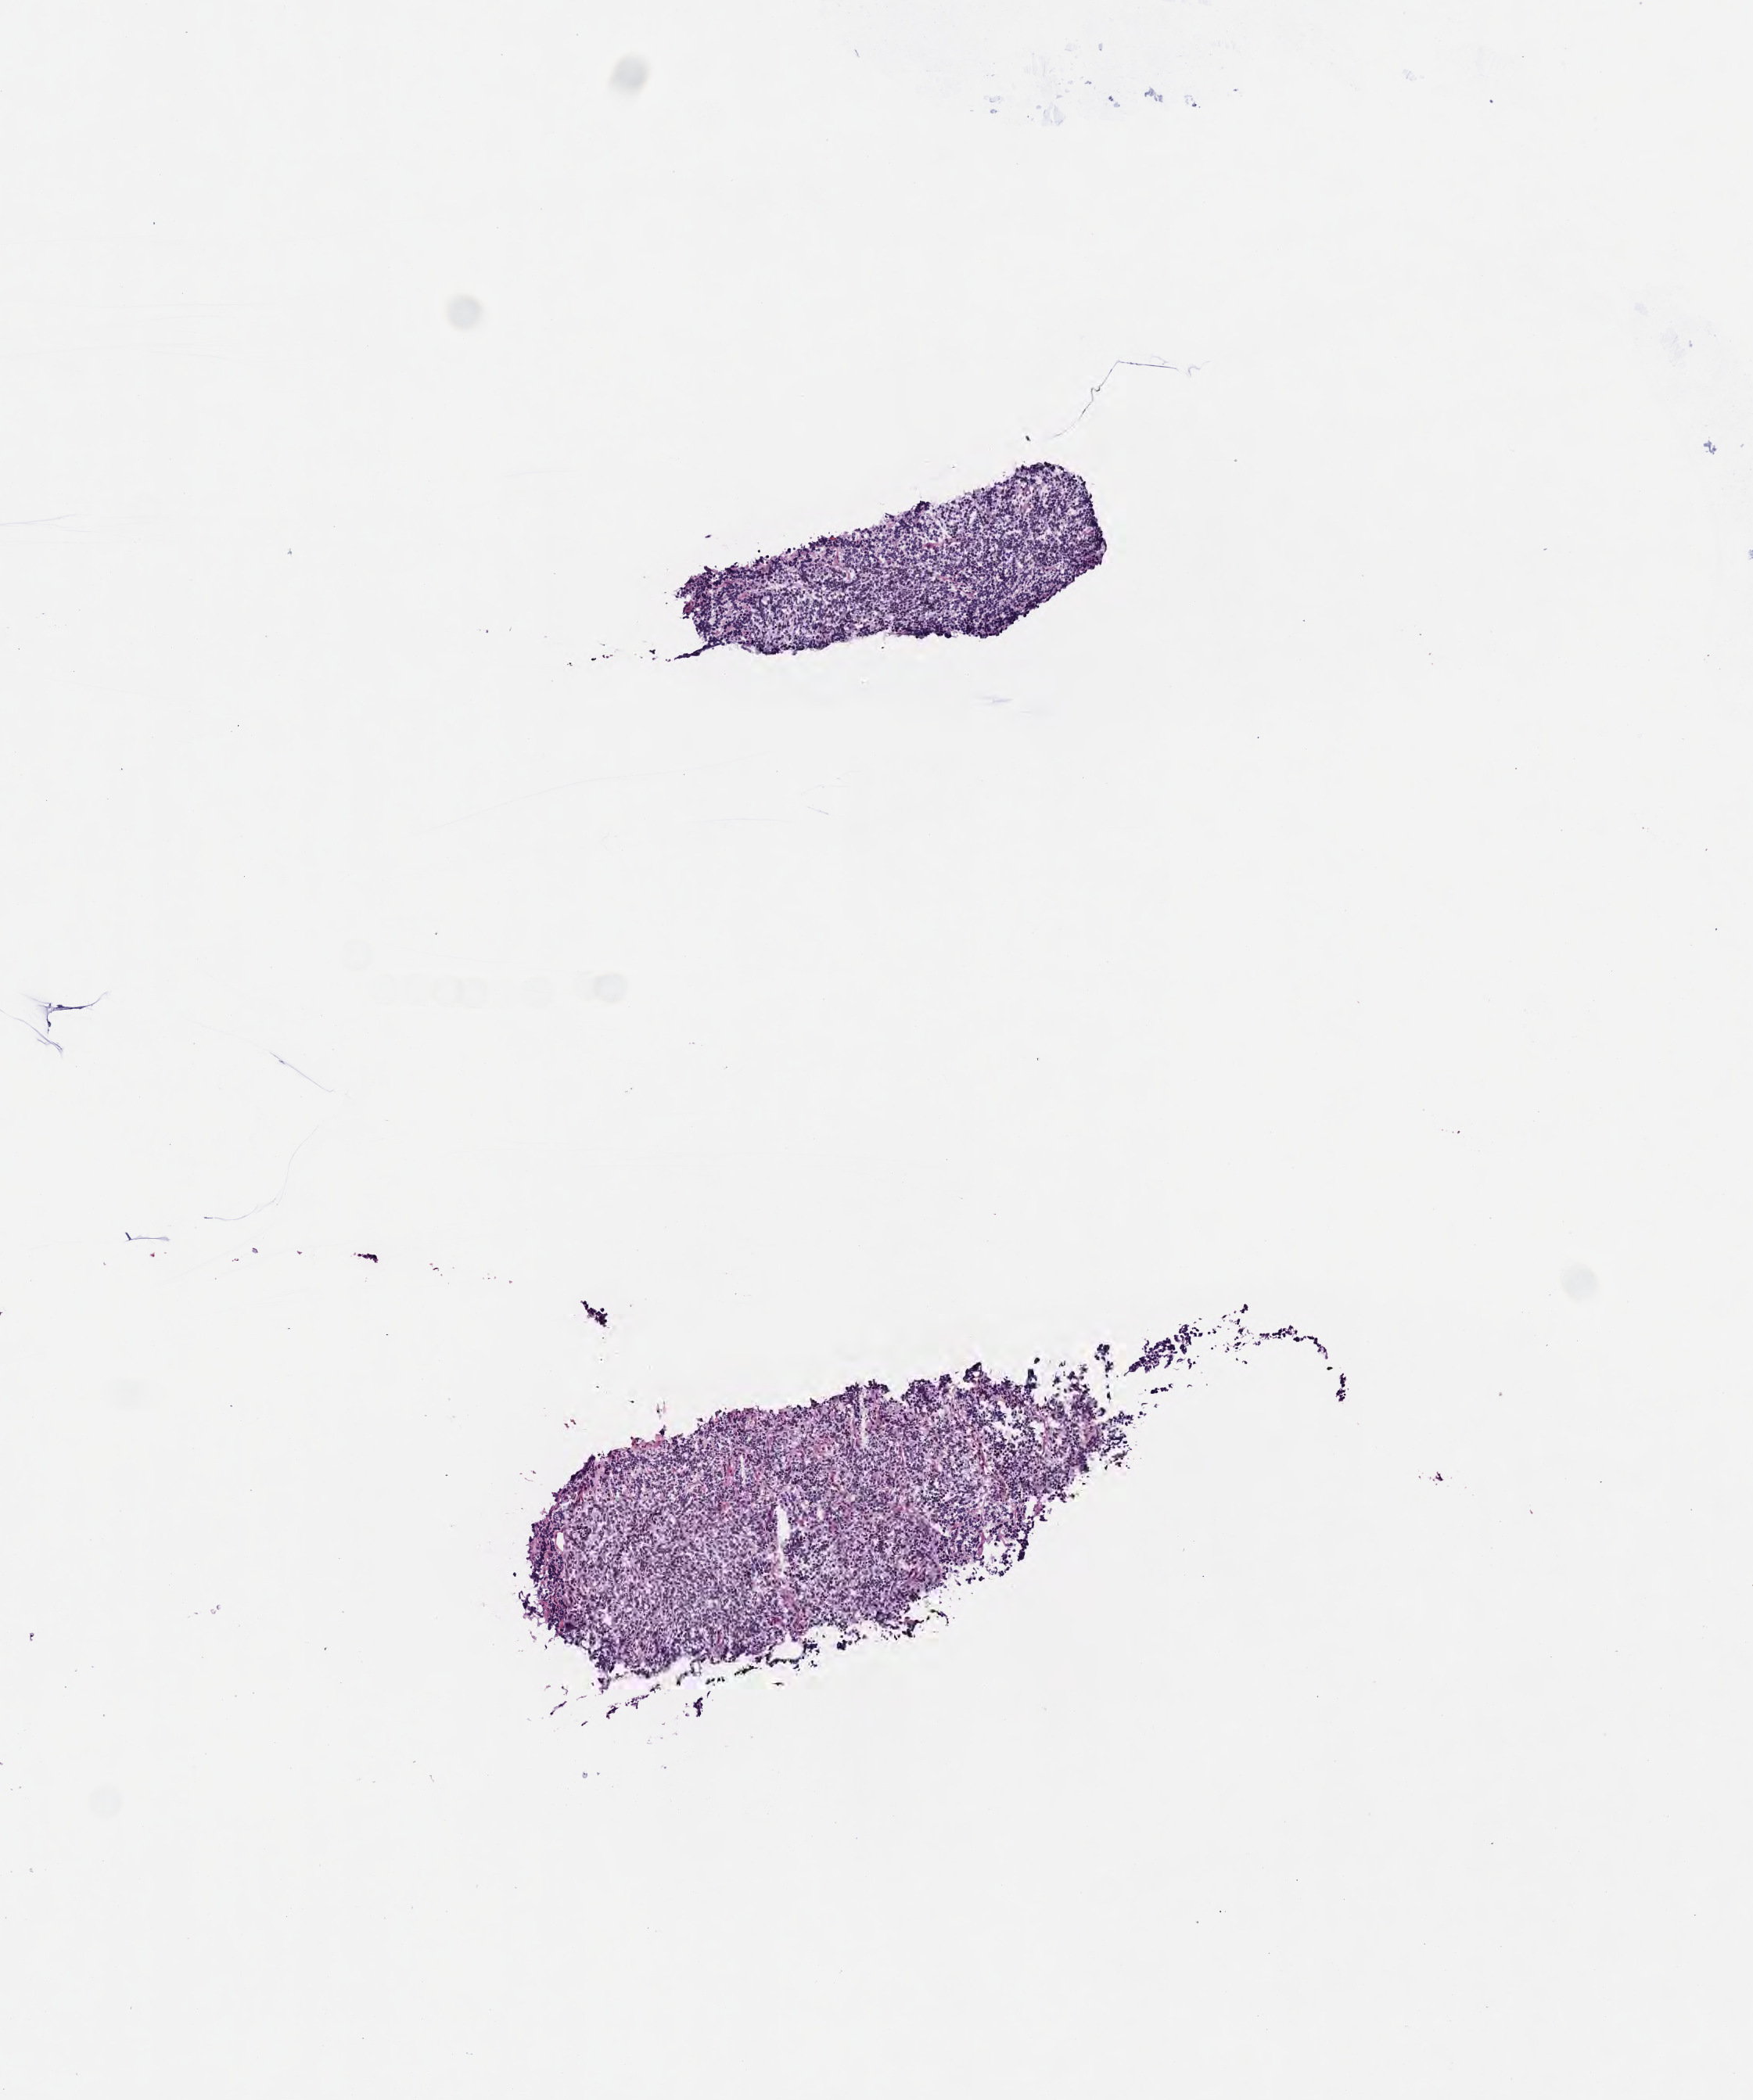
Whole-slide image, H&E stain, low-resolution overview of the scanned area, about 4.5 x 5.4 mm; frozen section; specimen: primary tumor; site: liver. Patient: male, age 15 years. Composition of this section per pathologist review: tumor cells 95%, tumor nuclei 95%, stromal cells 2%, necrosis 3%, normal cells 0%. Infiltration values recorded for this section: lymphocyte infiltration 15%, monocyte infiltration 30%, neutrophil infiltration 10%.
Diagnosis: Burkitt lymphoma, NOS. Section: top of the tissue portion. Ann Arbor stage (patient): Stage IV.